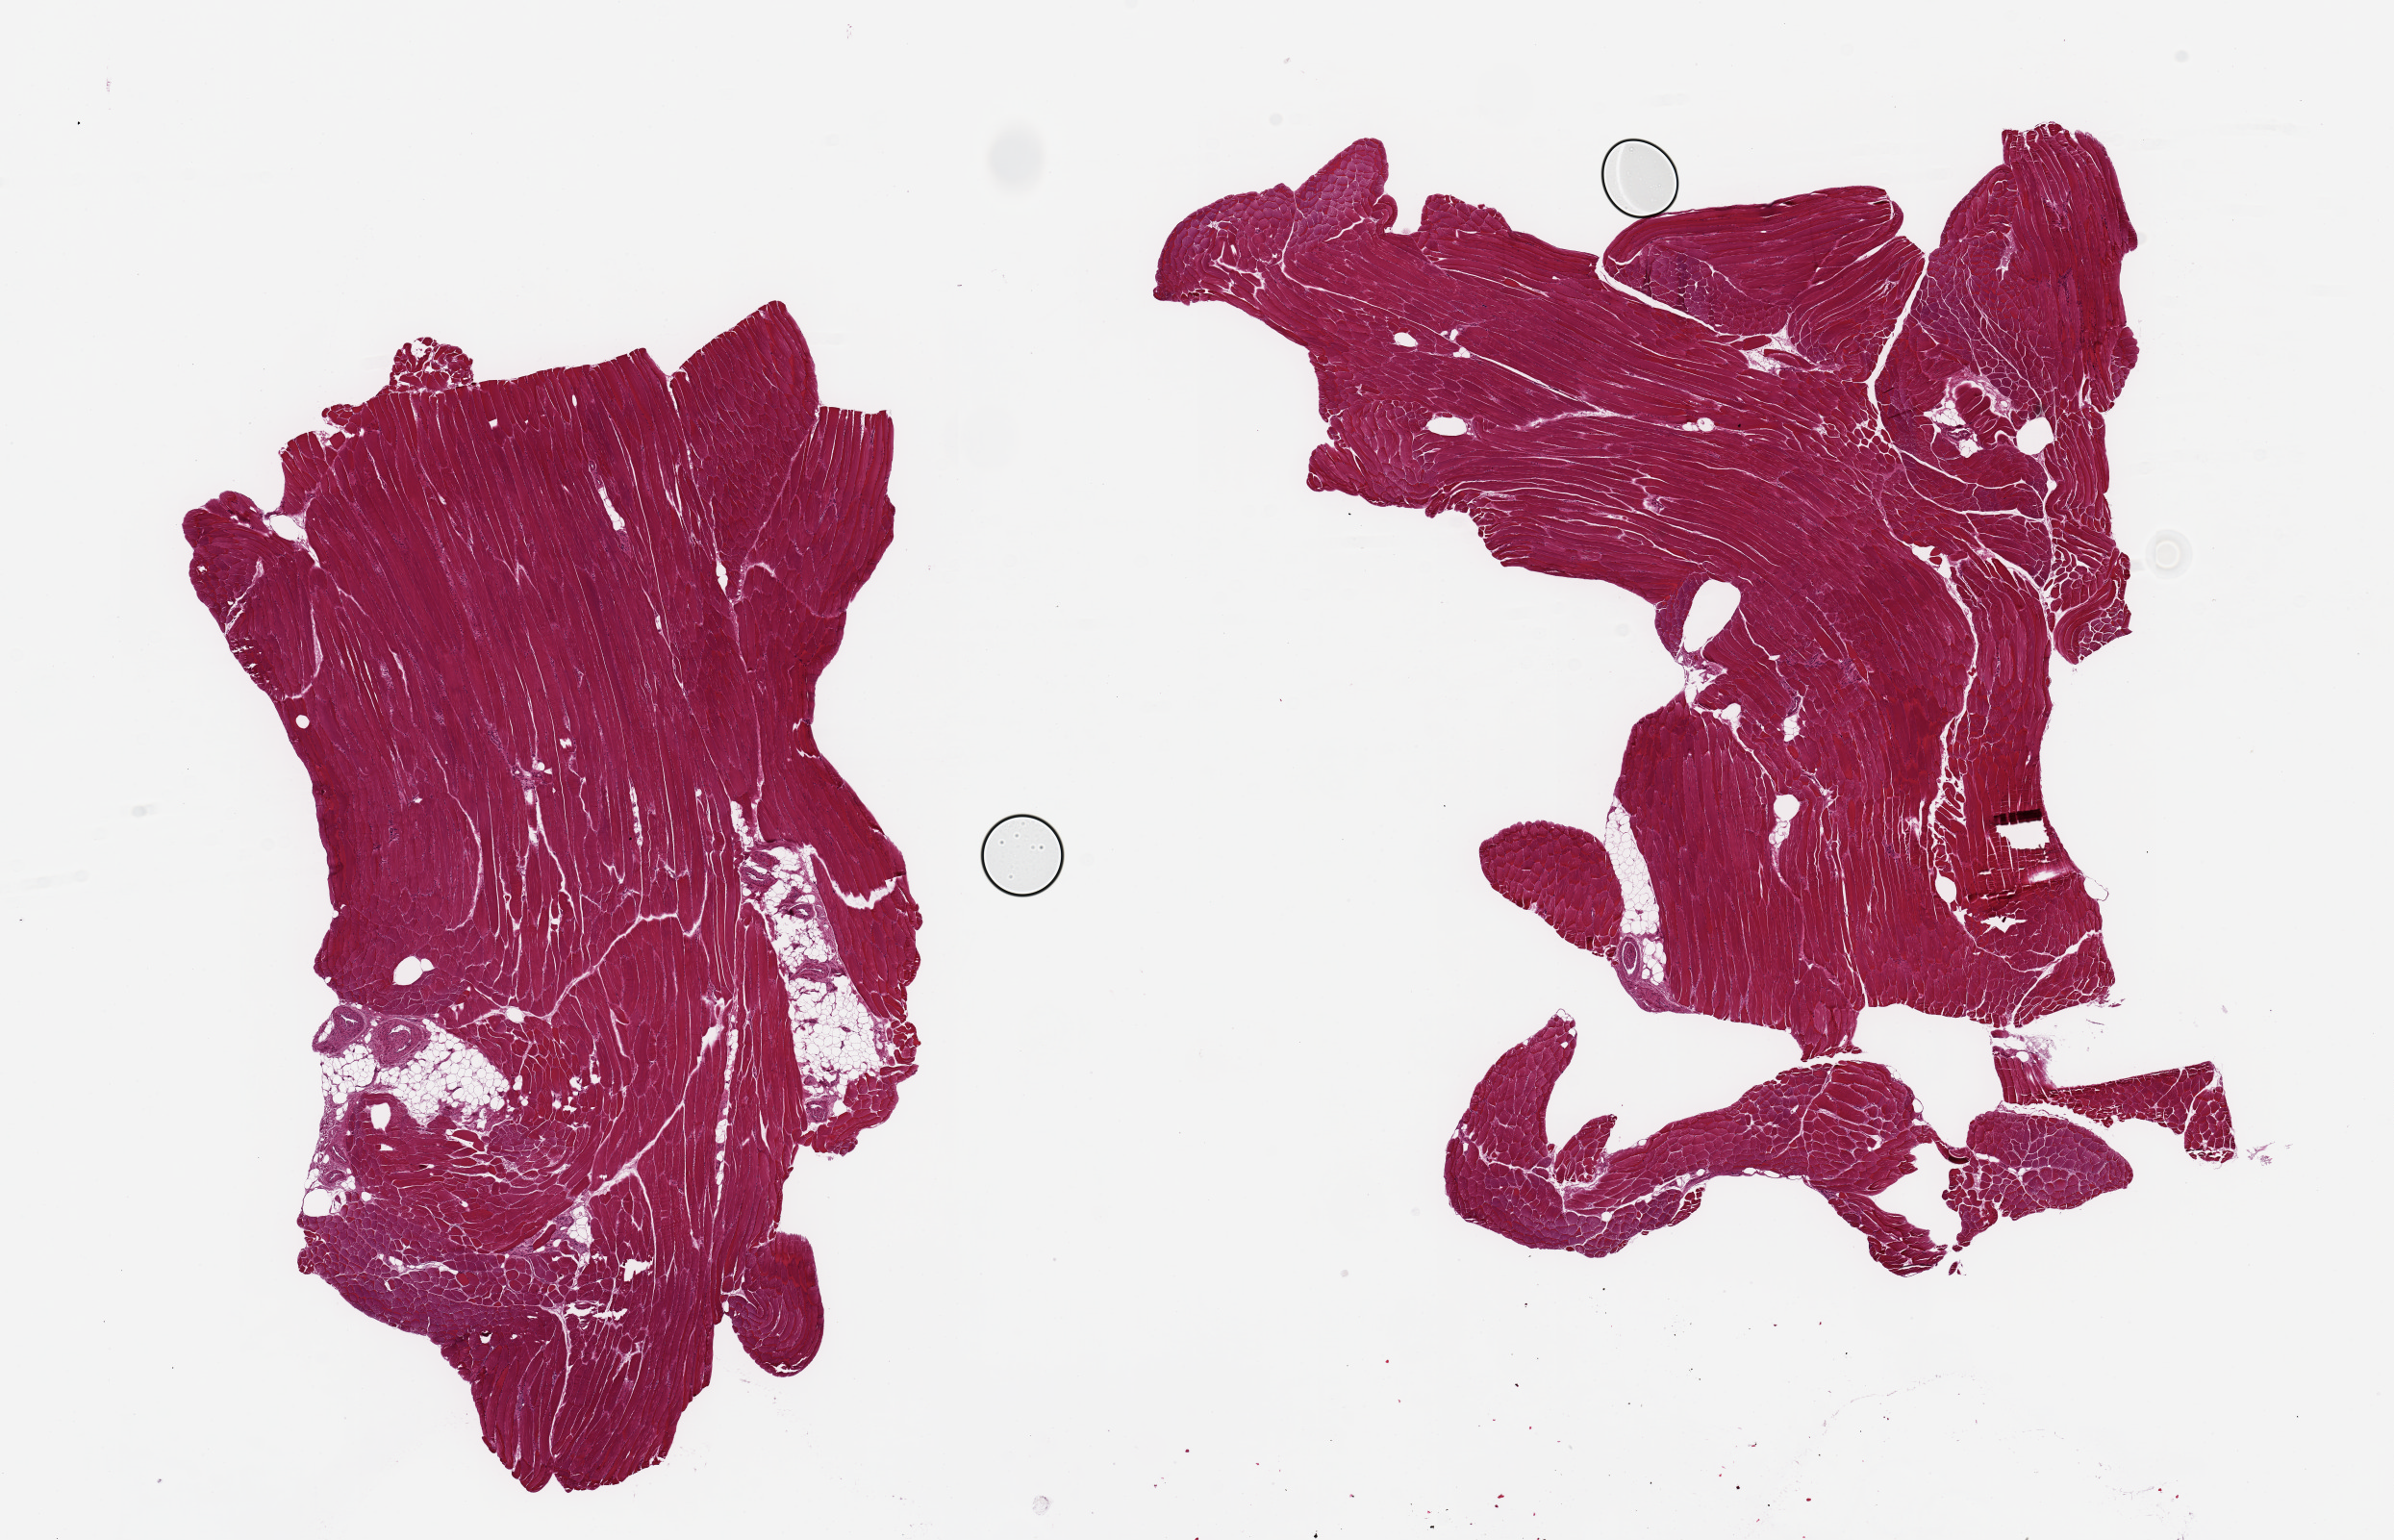
Haematoxylin and eosin whole-slide image, brightfield, low-resolution overview of the scanned area, about 19.7 x 12.7 mm (from a 20x scan). PAXgene-fixed, paraffin-embedded tissue. Target tissue: skeletal muscle. Tissue donor sample. Donor: male.
• pathologist's review note for this sample: 2 pieces 9.5x6 & 10x9mm; less than ~5% interstitial fat